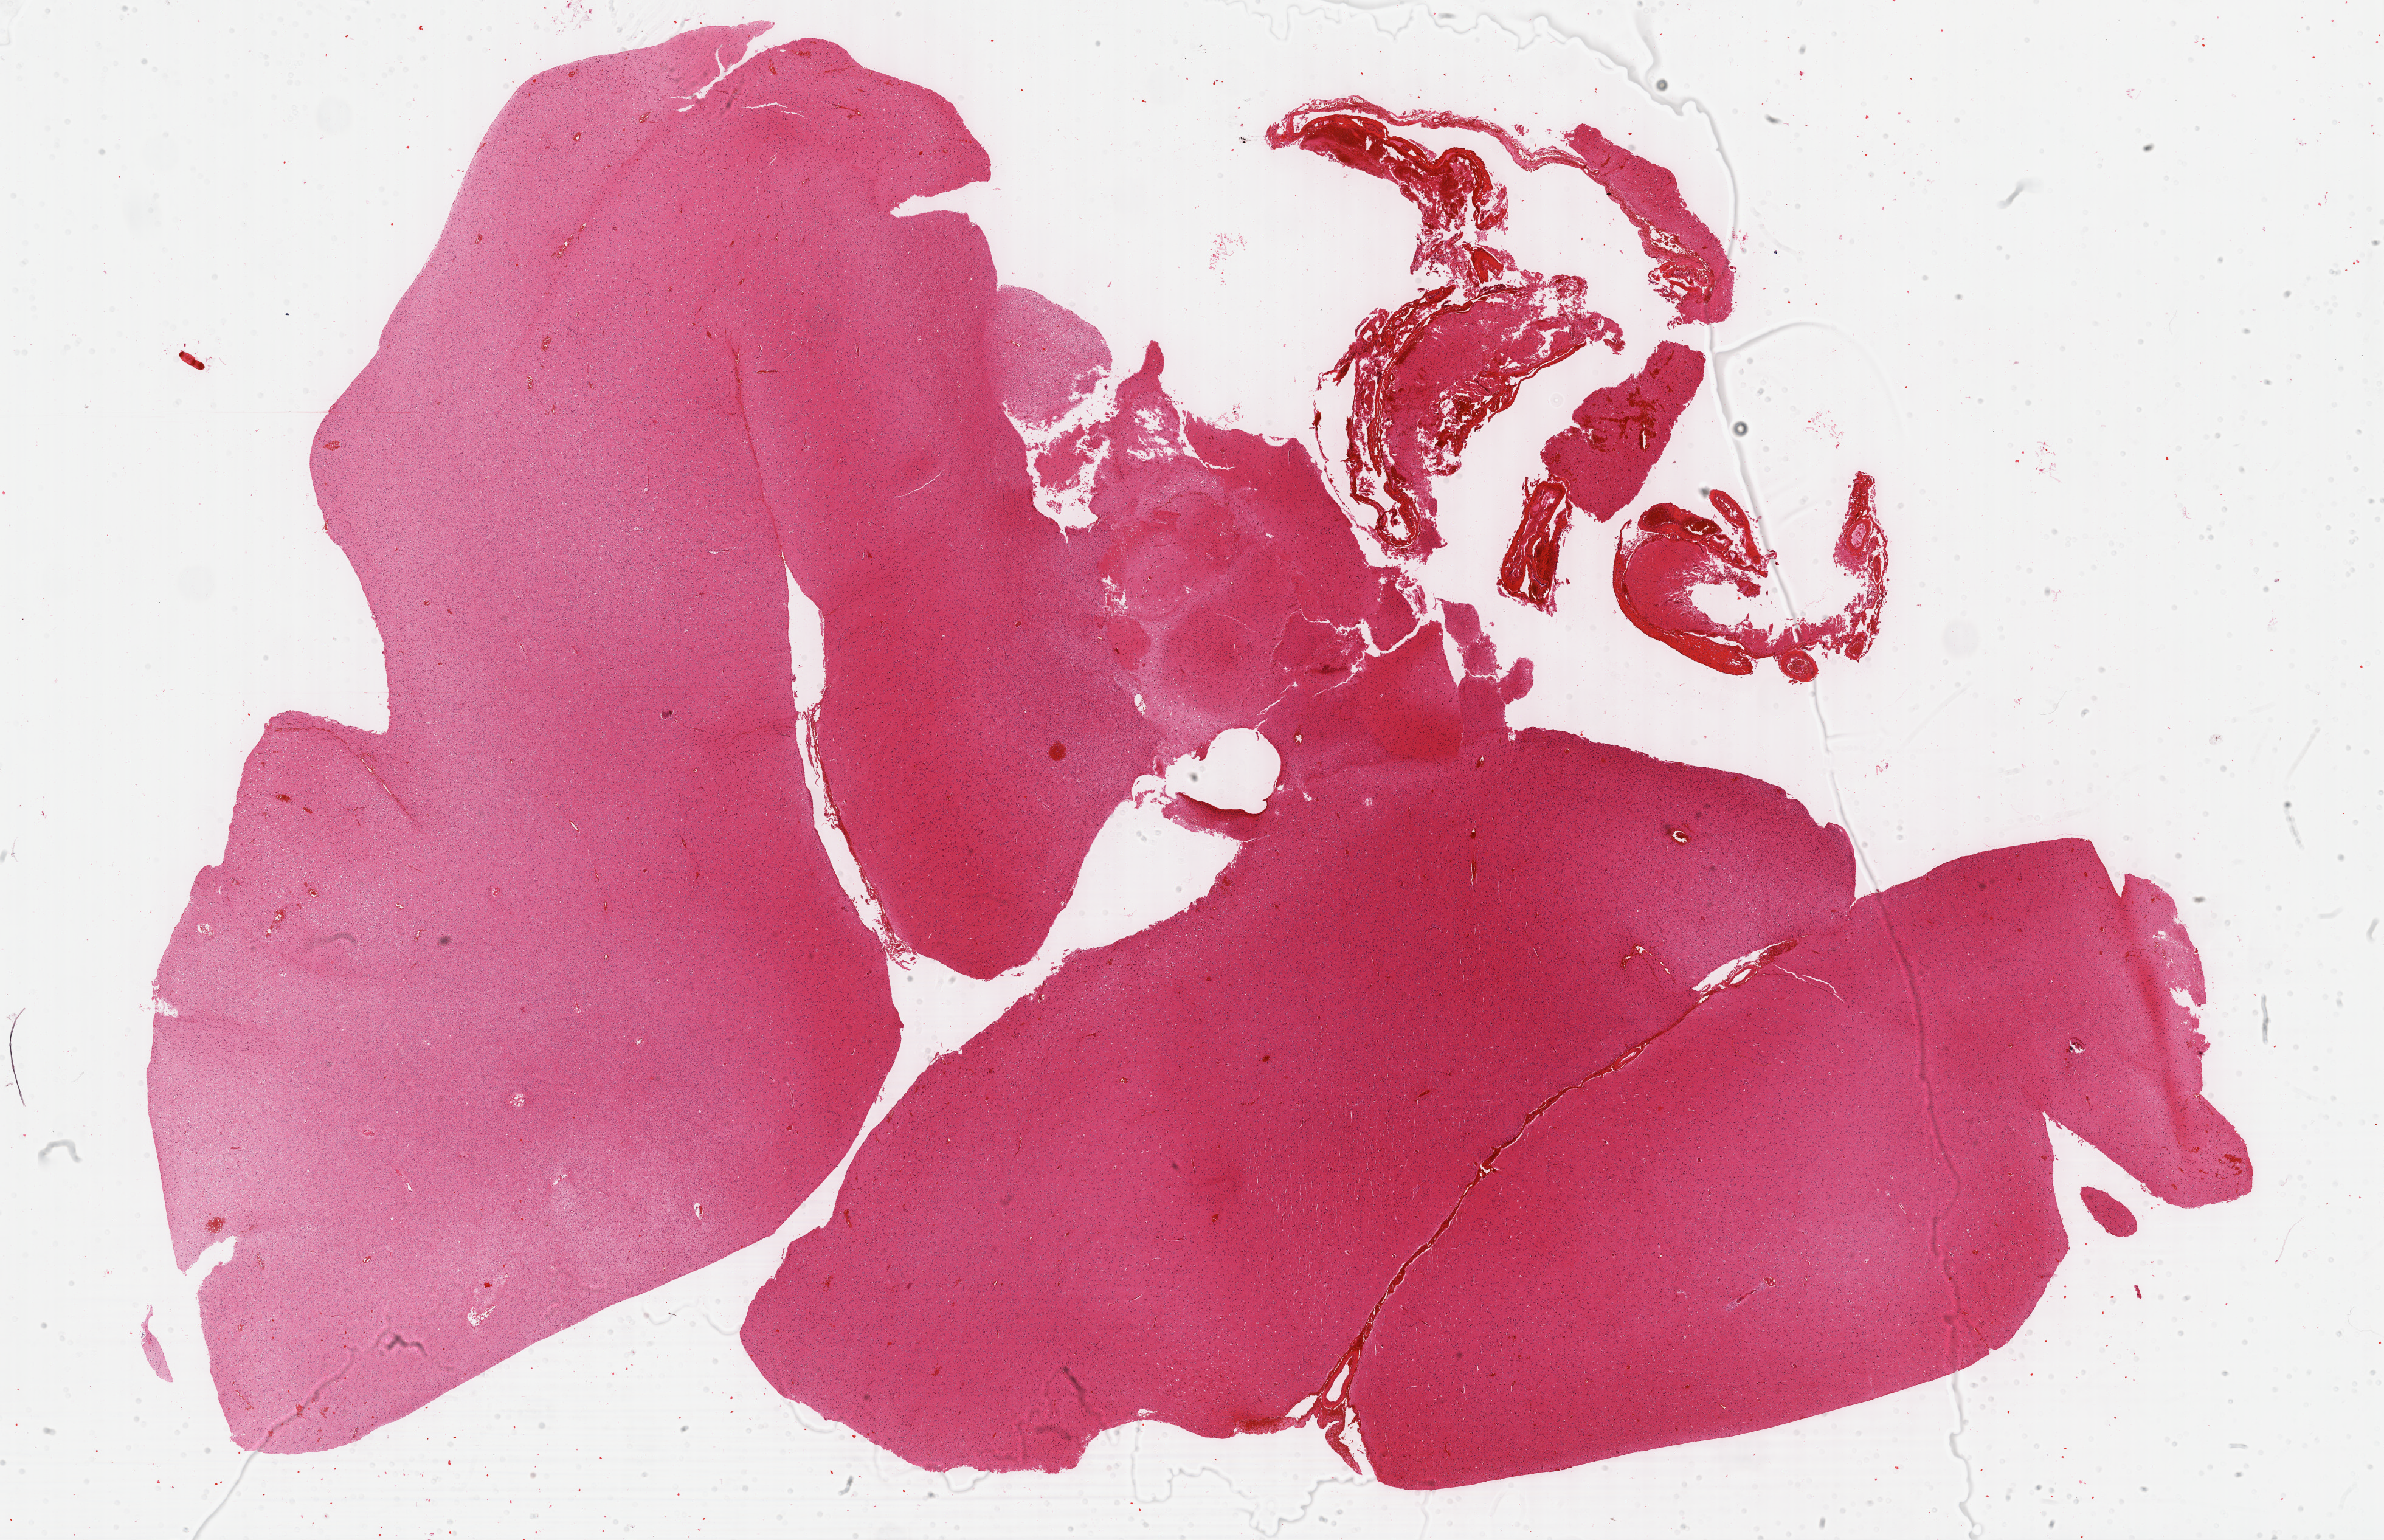
H&E-stained whole-slide image, whole scanned area (about 31.7 x 20.5 mm, acquisition: 40x scan) shown as a low-resolution overview, FFPE section, primary tumour sample from the brain. Patient: female, age at initial diagnosis 45 years. Histologic grade: G2 (moderately differentiated).
• histologic diagnosis: Mixed glioma